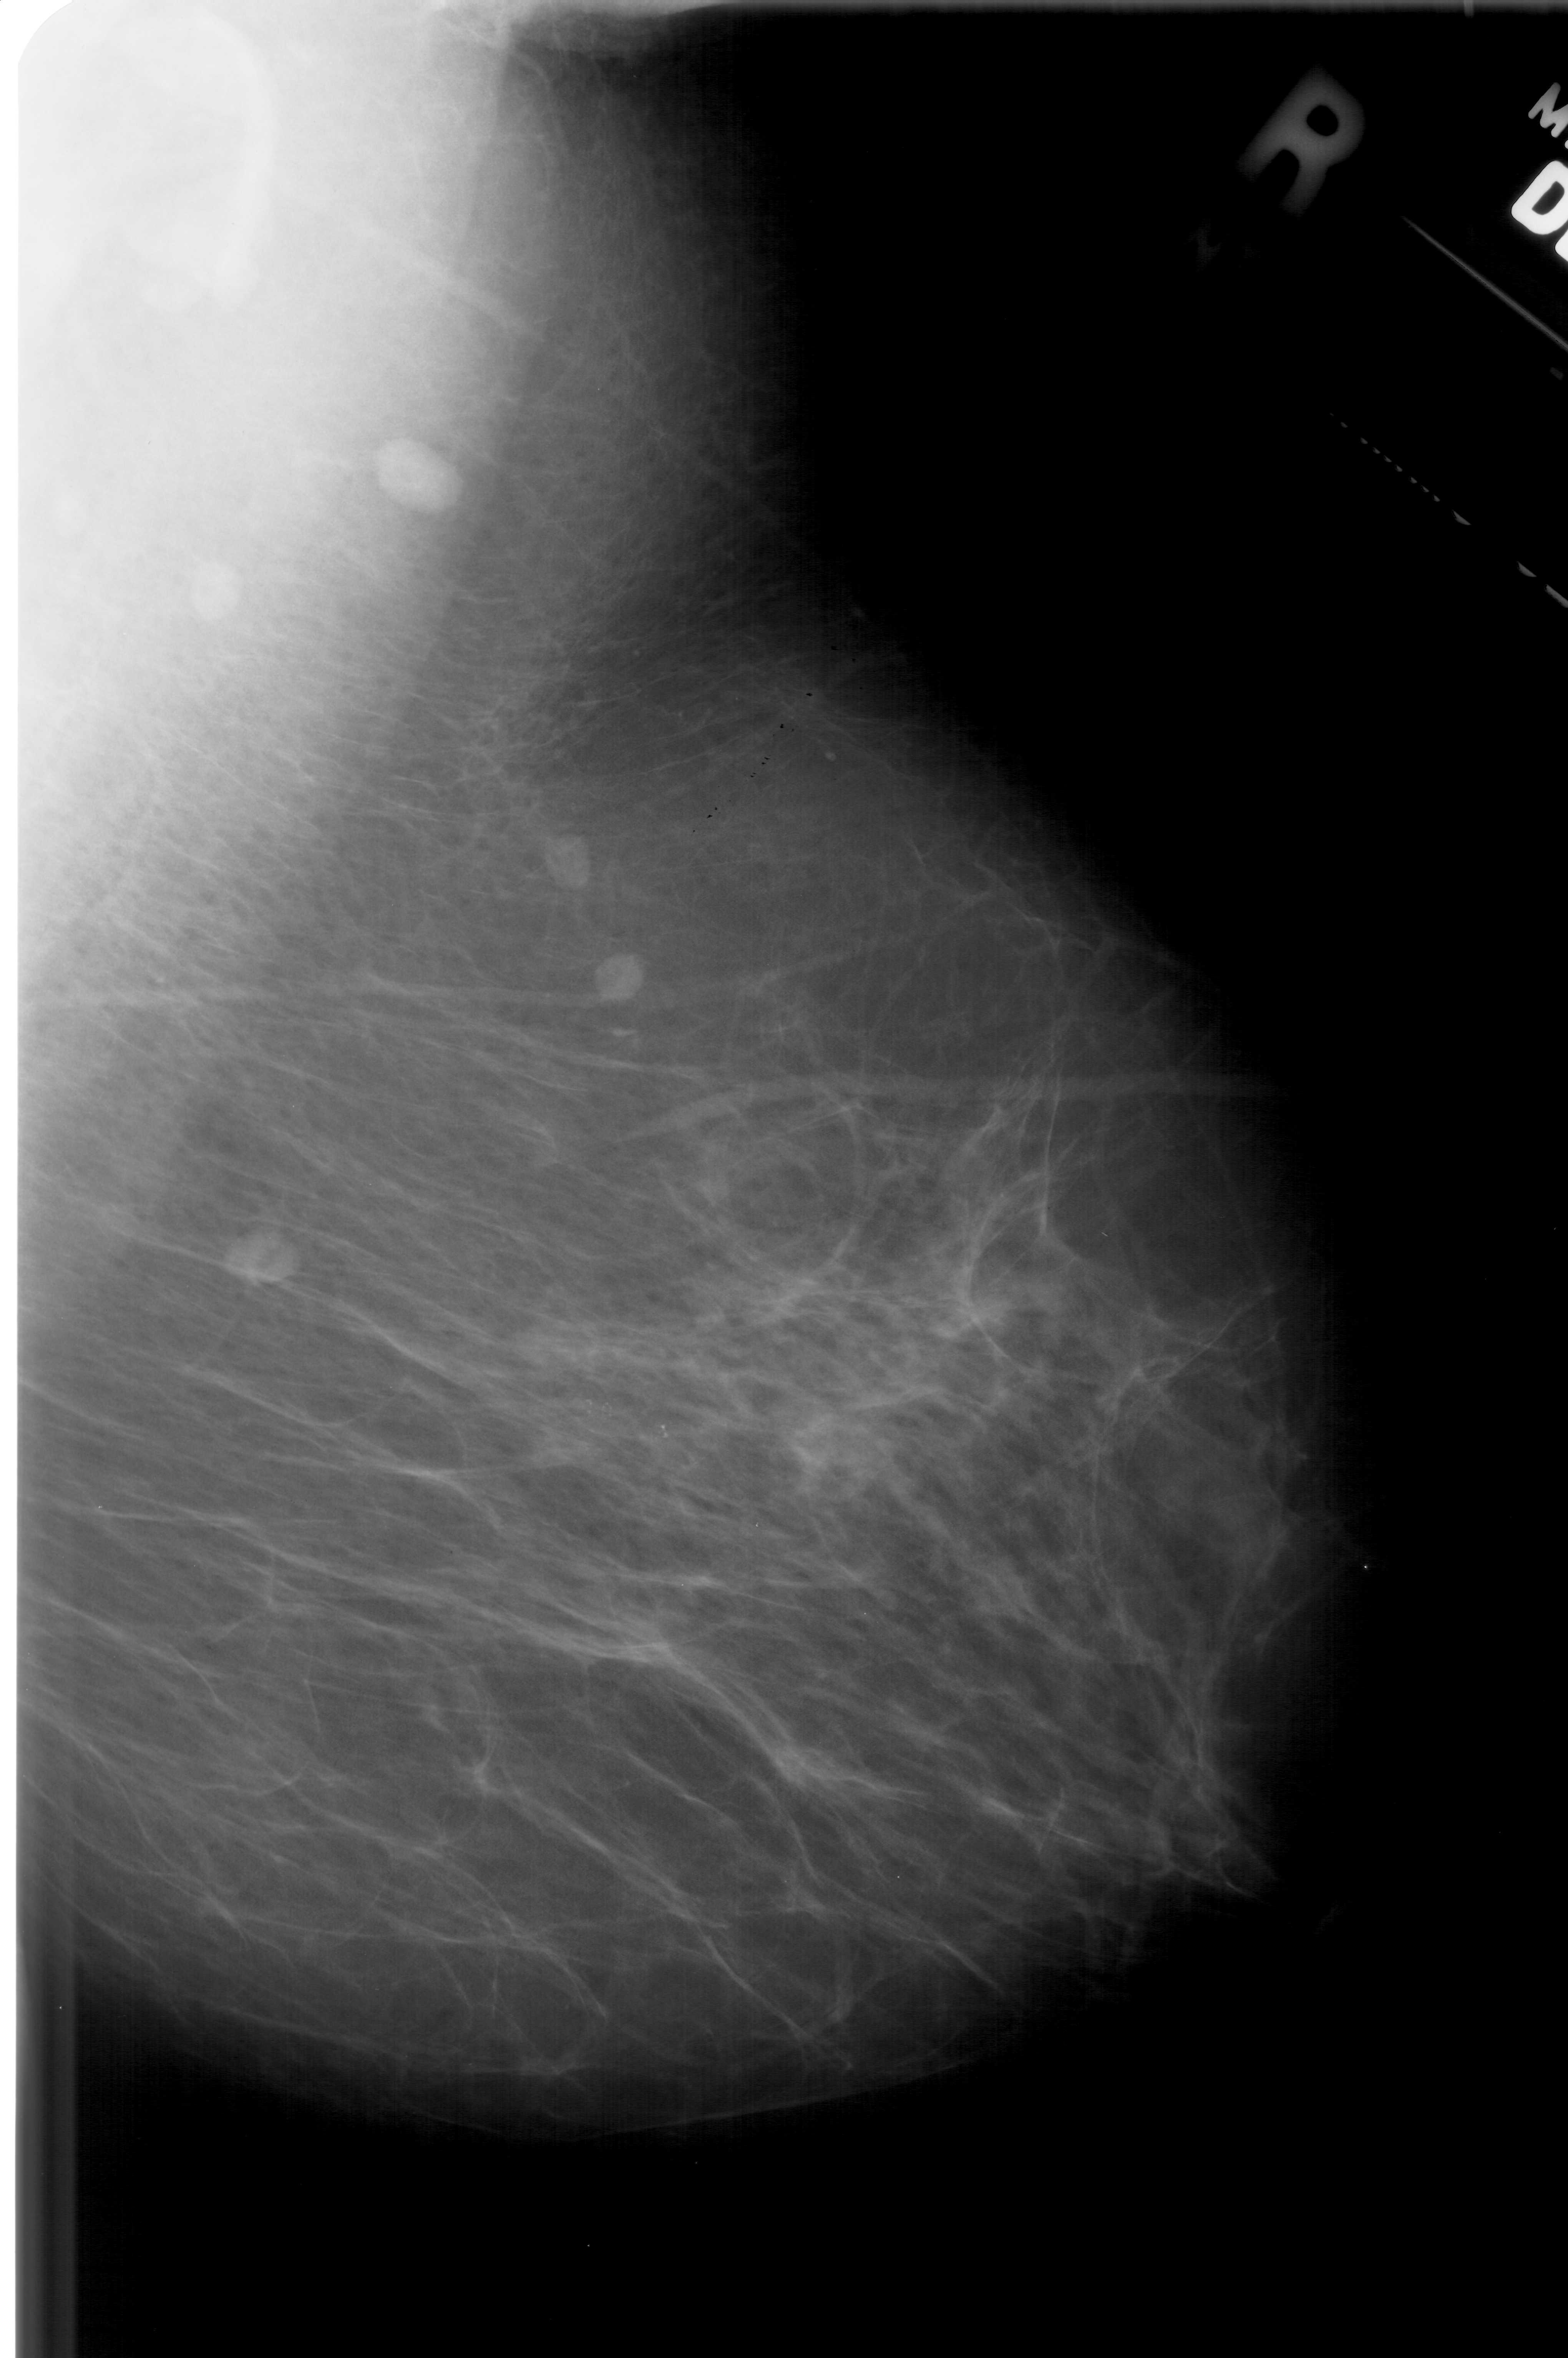
Digitized screen-film mammogram; right breast; MLO view; BI-RADS breast density category 2 (scale 1–4).
Radiologist-marked abnormalities on this image: calcifications, morphology pleomorphic, distribution clustered; BI-RADS assessment category 4; subtlety rating 3 on a 1 (subtle) to 5 (obvious) scale; pathology result (as recorded, not read from the image): benign.